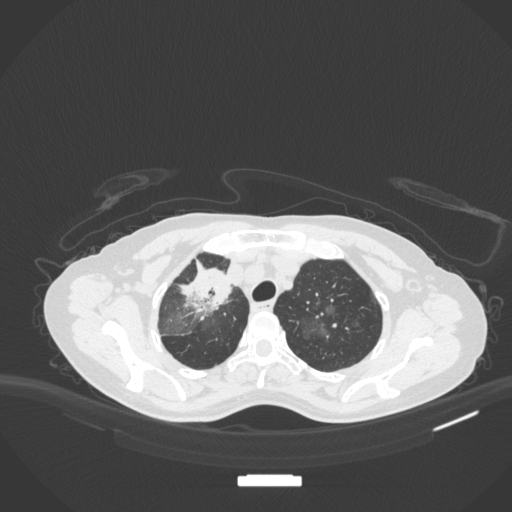
Chest CT, one axial slice. Slice 265 of 311 in the series (ordered by position). Reconstruction kernel B31f. 120 kVp. Lung window (W 1500 / L -600 HU). 1 mm slice thickness. 512 × 512 image matrix, field of view 400 × 400 mm. Female patient, age 59 years. Case-level facts recorded for this patient, not image findings: clinical TNM (as recorded): T3 N0 M0.
Annotated regions visible in this slice (bounding box drawn by a radiologist):
- lung tumour (recorded histology: adenocarcinoma): bounding box [x1, y1, x2, y2] px = [177, 259, 232, 319]